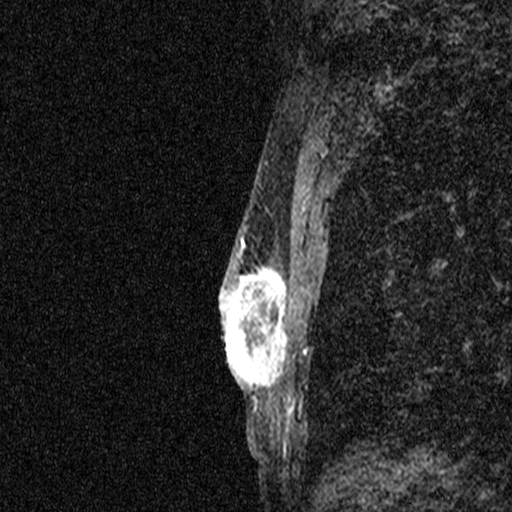
Breast MRI (dynamic contrast-enhanced), one sagittal slice. Position 28 of 44 along the scan axis. Dynamic contrast-enhanced study with each time point stored as its own series, time point 2 of 3 at this slice position (early post-contrast, ordered by acquisition time). 1.5 T. TE 4.5 ms, TR 11 ms. 2.05 mm slice thickness. 512 × 512 image matrix. Patient: female, 44 years. From the clinical record (not read from this slice): setting: breast cancer imaged before/during neoadjuvant chemotherapy; receptor status: HR-positive, HER2-negative.
Structures marked on this image (semi-automatically segmented with operator editing):
- analysis volume of interest (the breast-tissue region the enhancement analysis was run in; not a lesion): box from (x=204, y=254) to (x=291, y=401) px
- tumour enhancement mask (voxels above the 90 % enhancement threshold inside the analysis volume of interest): (x=219, y=254)–(x=287, y=400)